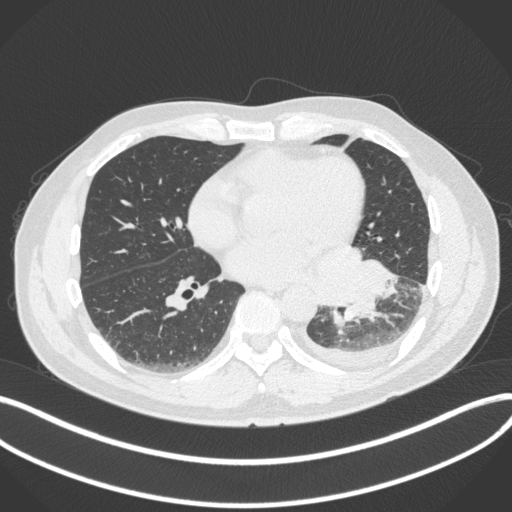
Chest CT, one axial slice; slice 152 of 350 in the series (ordered by position); 120 kVp; lung window (W 1500 / L -600 HU); 1 mm slice thickness; 512 × 512 image matrix, field of view 400 × 400 mm. Patient: male, 58 years. Case-level facts recorded for this patient, not image findings: clinical TNM (as recorded): T3 N1 M1b; histopathological grade: G3.
Outlined on this slice (bounding box drawn by a radiologist):
- lung tumour (recorded histology: small cell carcinoma): box from (x=344, y=252) to (x=402, y=328) px